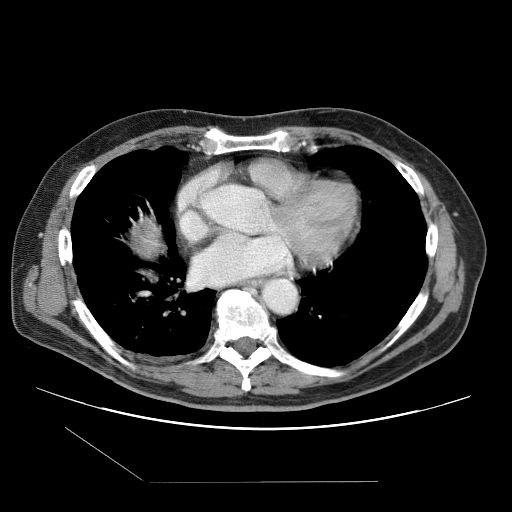
Contrast-enhanced abdominal CT (liver protocol), one axial slice; position 105 of 109 along the scan axis; one of 2 acquisitions stored at this slice position; soft-tissue window (W 400 / L 40 HU); 2.5 mm slice thickness; 512 × 512 image matrix. From the clinical record (not read from this slice): diagnosis: hepatocellular carcinoma (patient treated with transarterial chemoembolisation; whether this scan precedes or follows treatment is not stated here); TNM stage (as recorded): Stage-IIIB; Child-Pugh class: A; tumour differentiation: well differentiated.
Structures marked on this image (semi-automatic segmentation, software-assisted and operator-edited):
- liver parenchyma outside the tumour (the mass and vessels are separate outlines, so this box may not span the whole liver): bounding box (x1, y1, x2, y2) in pixels: (132, 220, 164, 258)